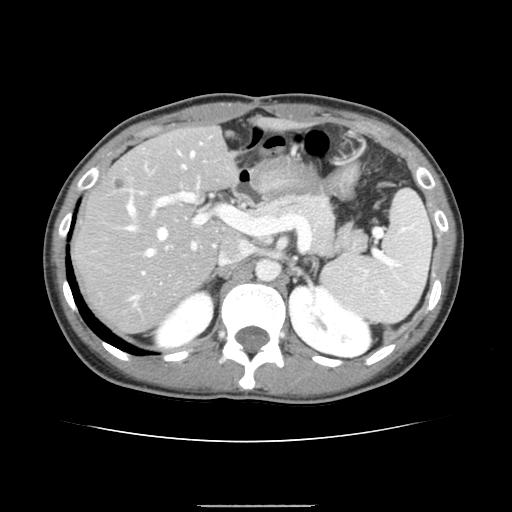
Contrast-enhanced abdominal CT, one axial slice. Slice 94 of 150 in the series (ordered by position). 120 kVp. Intravenous contrast given. Soft-tissue window (W 400 / L 40 HU). 512 × 512 image matrix, field of view 324 × 324 mm. Female patient, age 32 years. Case-level facts recorded for this patient, not image findings: diagnosis: colorectal cancer liver metastases, imaged before liver resection; multiple liver metastases: yes; largest metastasis: 0.7 cm; disease in both lobes: no.
Structures marked on this image (manually delineated by an expert):
- hepatic veins: bounding box [x1, y1, x2, y2] px = [127, 152, 194, 298]
- liver: [74, 128, 237, 333]
- planned liver remnant (the part of the liver to remain after resection): [74, 128, 237, 279]
- portal vein (with intrahepatic branches): [129, 167, 234, 273]
- liver metastasis: [115, 181, 124, 190]